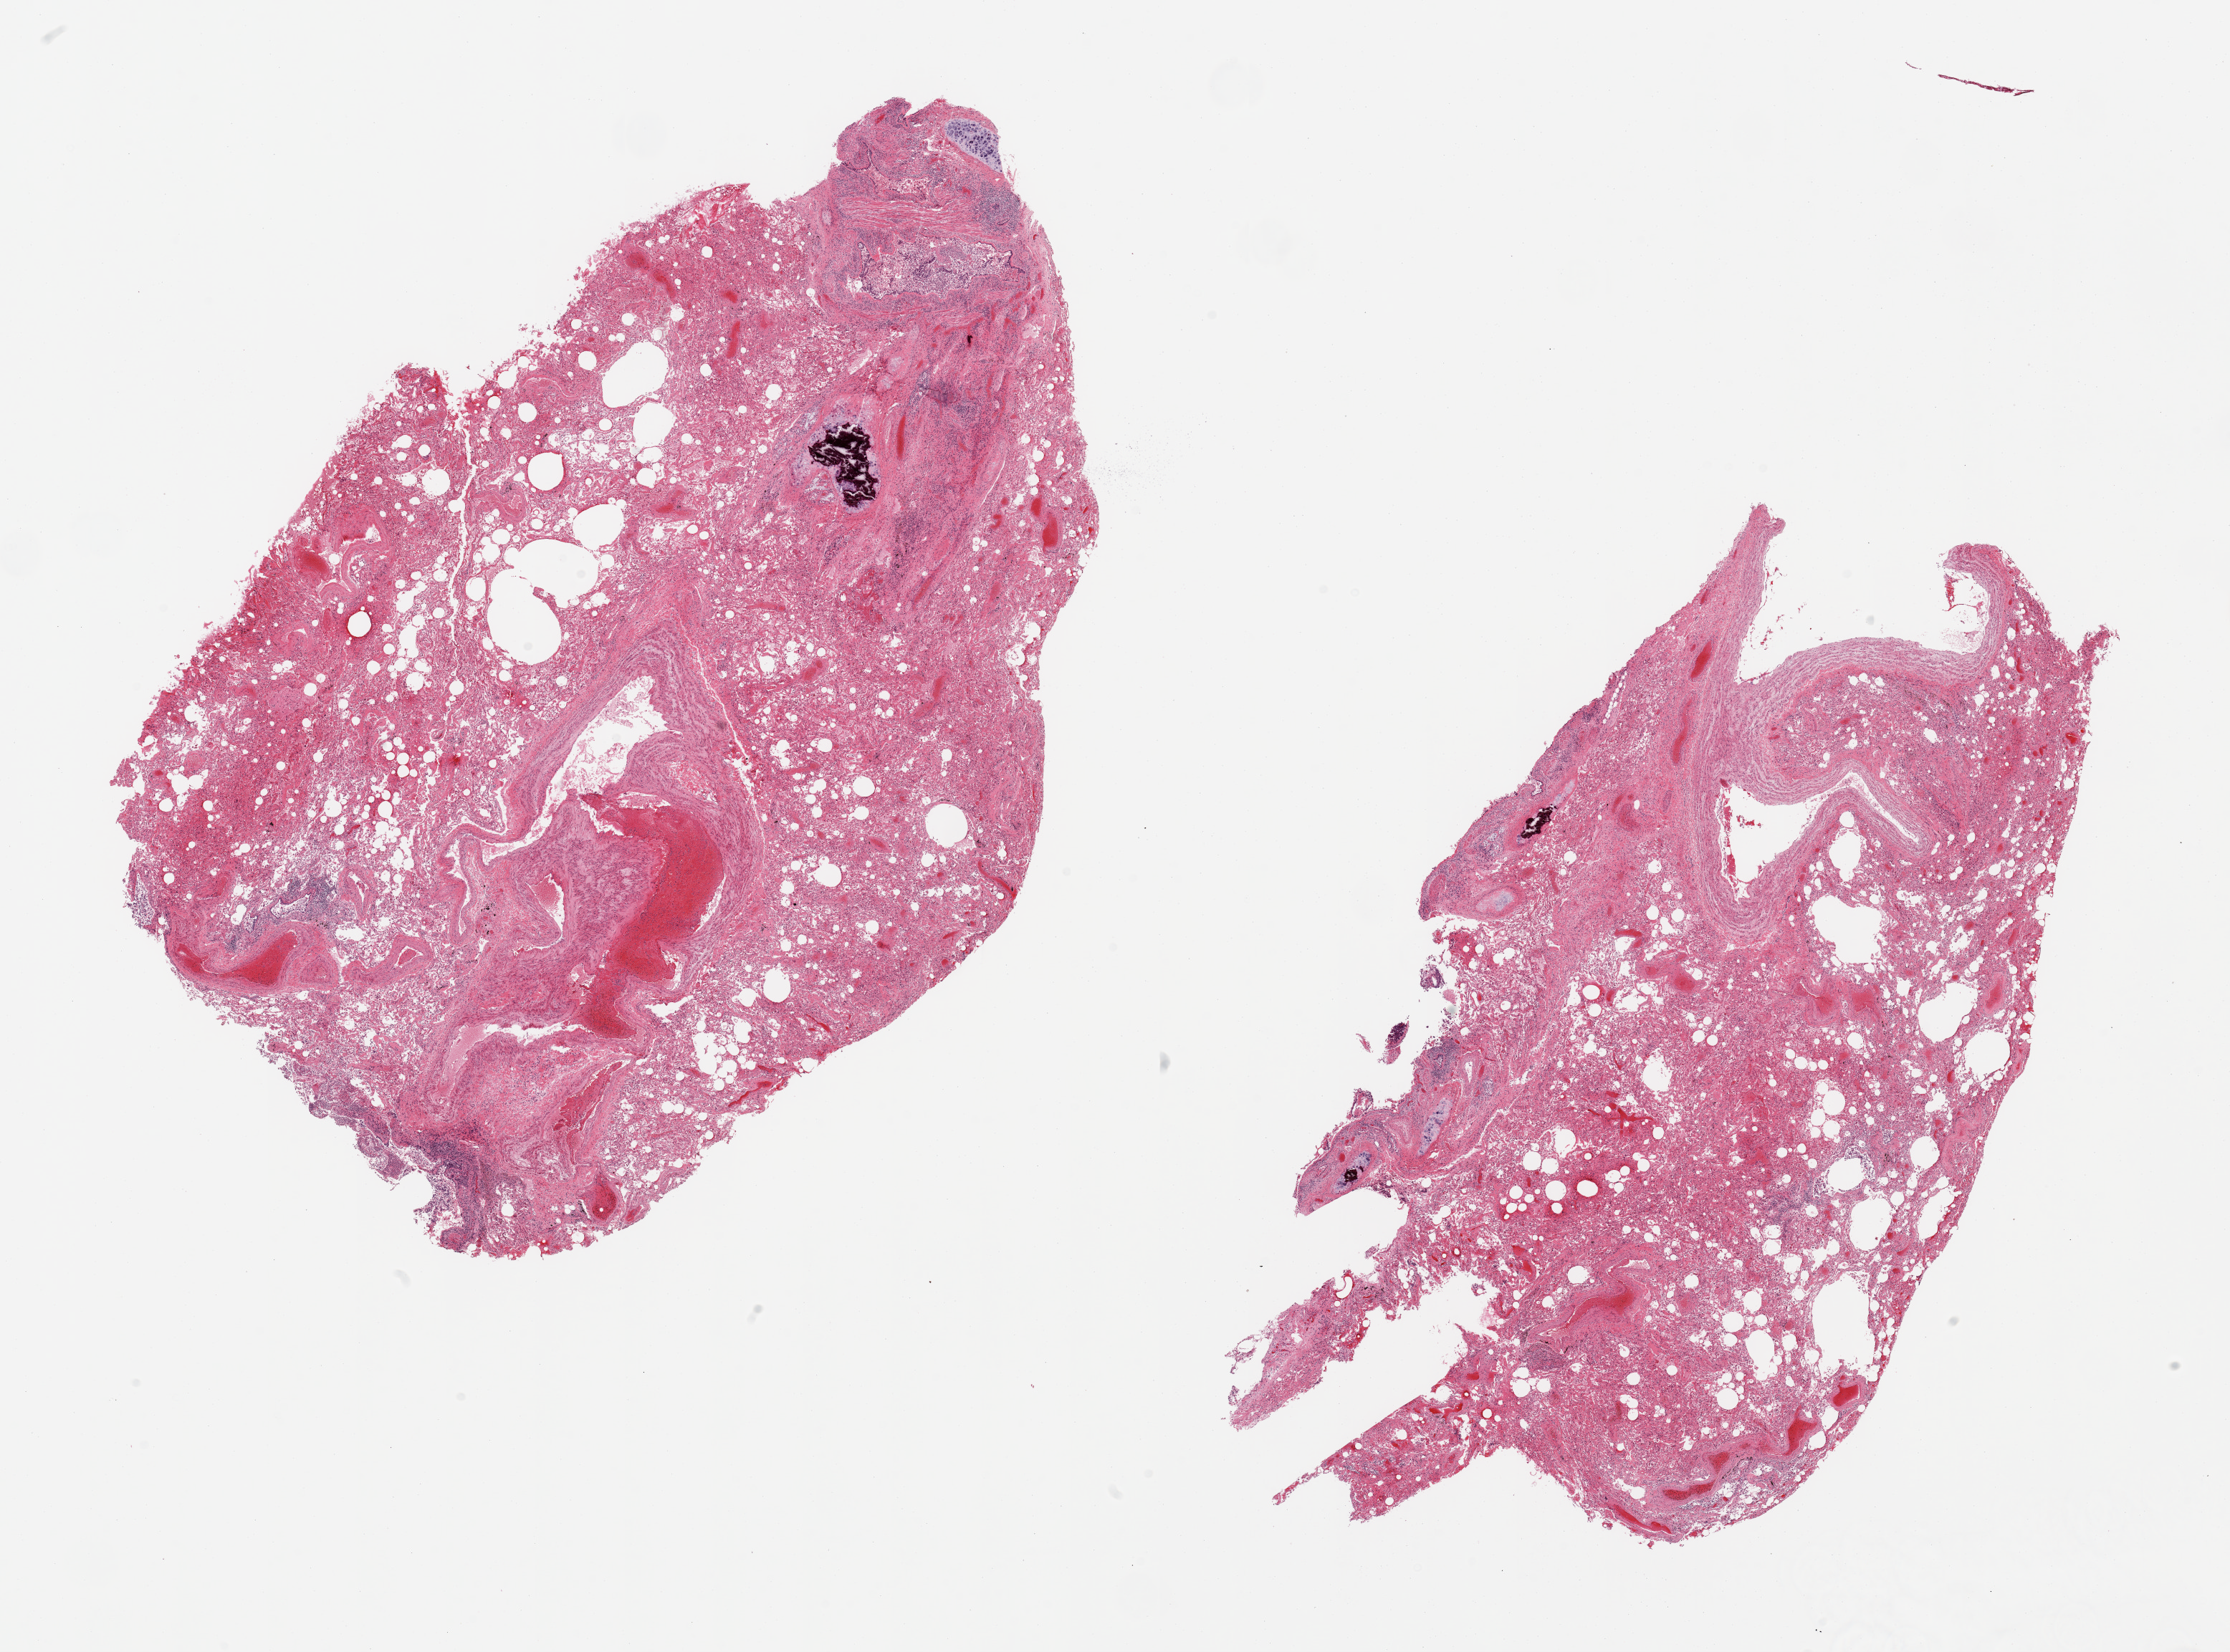
H&E whole-slide image, a low-resolution overview of the entire scanned area, about 24.6 x 18.2 mm. PAXgene-fixed paraffin-embedded (PFPE) section. Sampled site (target tissue): lung. Tissue donor sample. Donor sex: female.
Reviewer comment on this tissue sample: 2 pieces, moderate-severe congestion; Foci of bronchial hyaline cartilage noted, some with dystrophic calcificaiton.